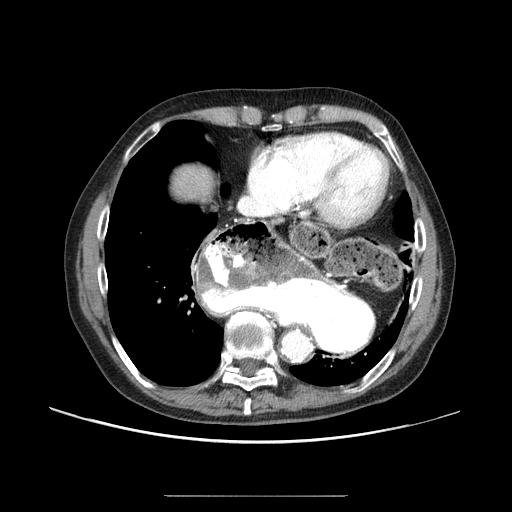
Contrast-enhanced abdominal CT (liver protocol), one axial slice. Position 81 of 91 along the scan axis. Reconstruction kernel STANDARD. 100 kVp. One of 2 acquisitions stored at this slice position. Soft-tissue window (W 400 / L 40 HU). 2.5 mm slice thickness. 512 × 512 image matrix, field of view 400 × 400 mm. From the clinical record (not read from this slice): diagnosis: hepatocellular carcinoma (patient treated with transarterial chemoembolisation; whether this scan precedes or follows treatment is not stated here); TNM stage (as recorded): Stage-I; Child-Pugh class: A; tumour differentiation: moderately differentiated; tumour nodularity: uninodular.
Structures marked on this image (semi-automatic segmentation, software-assisted and operator-edited):
- liver parenchyma outside the tumour (the mass and vessels are separate outlines, so this box may not span the whole liver): bounding box [x1, y1, x2, y2] px = [172, 166, 212, 198]